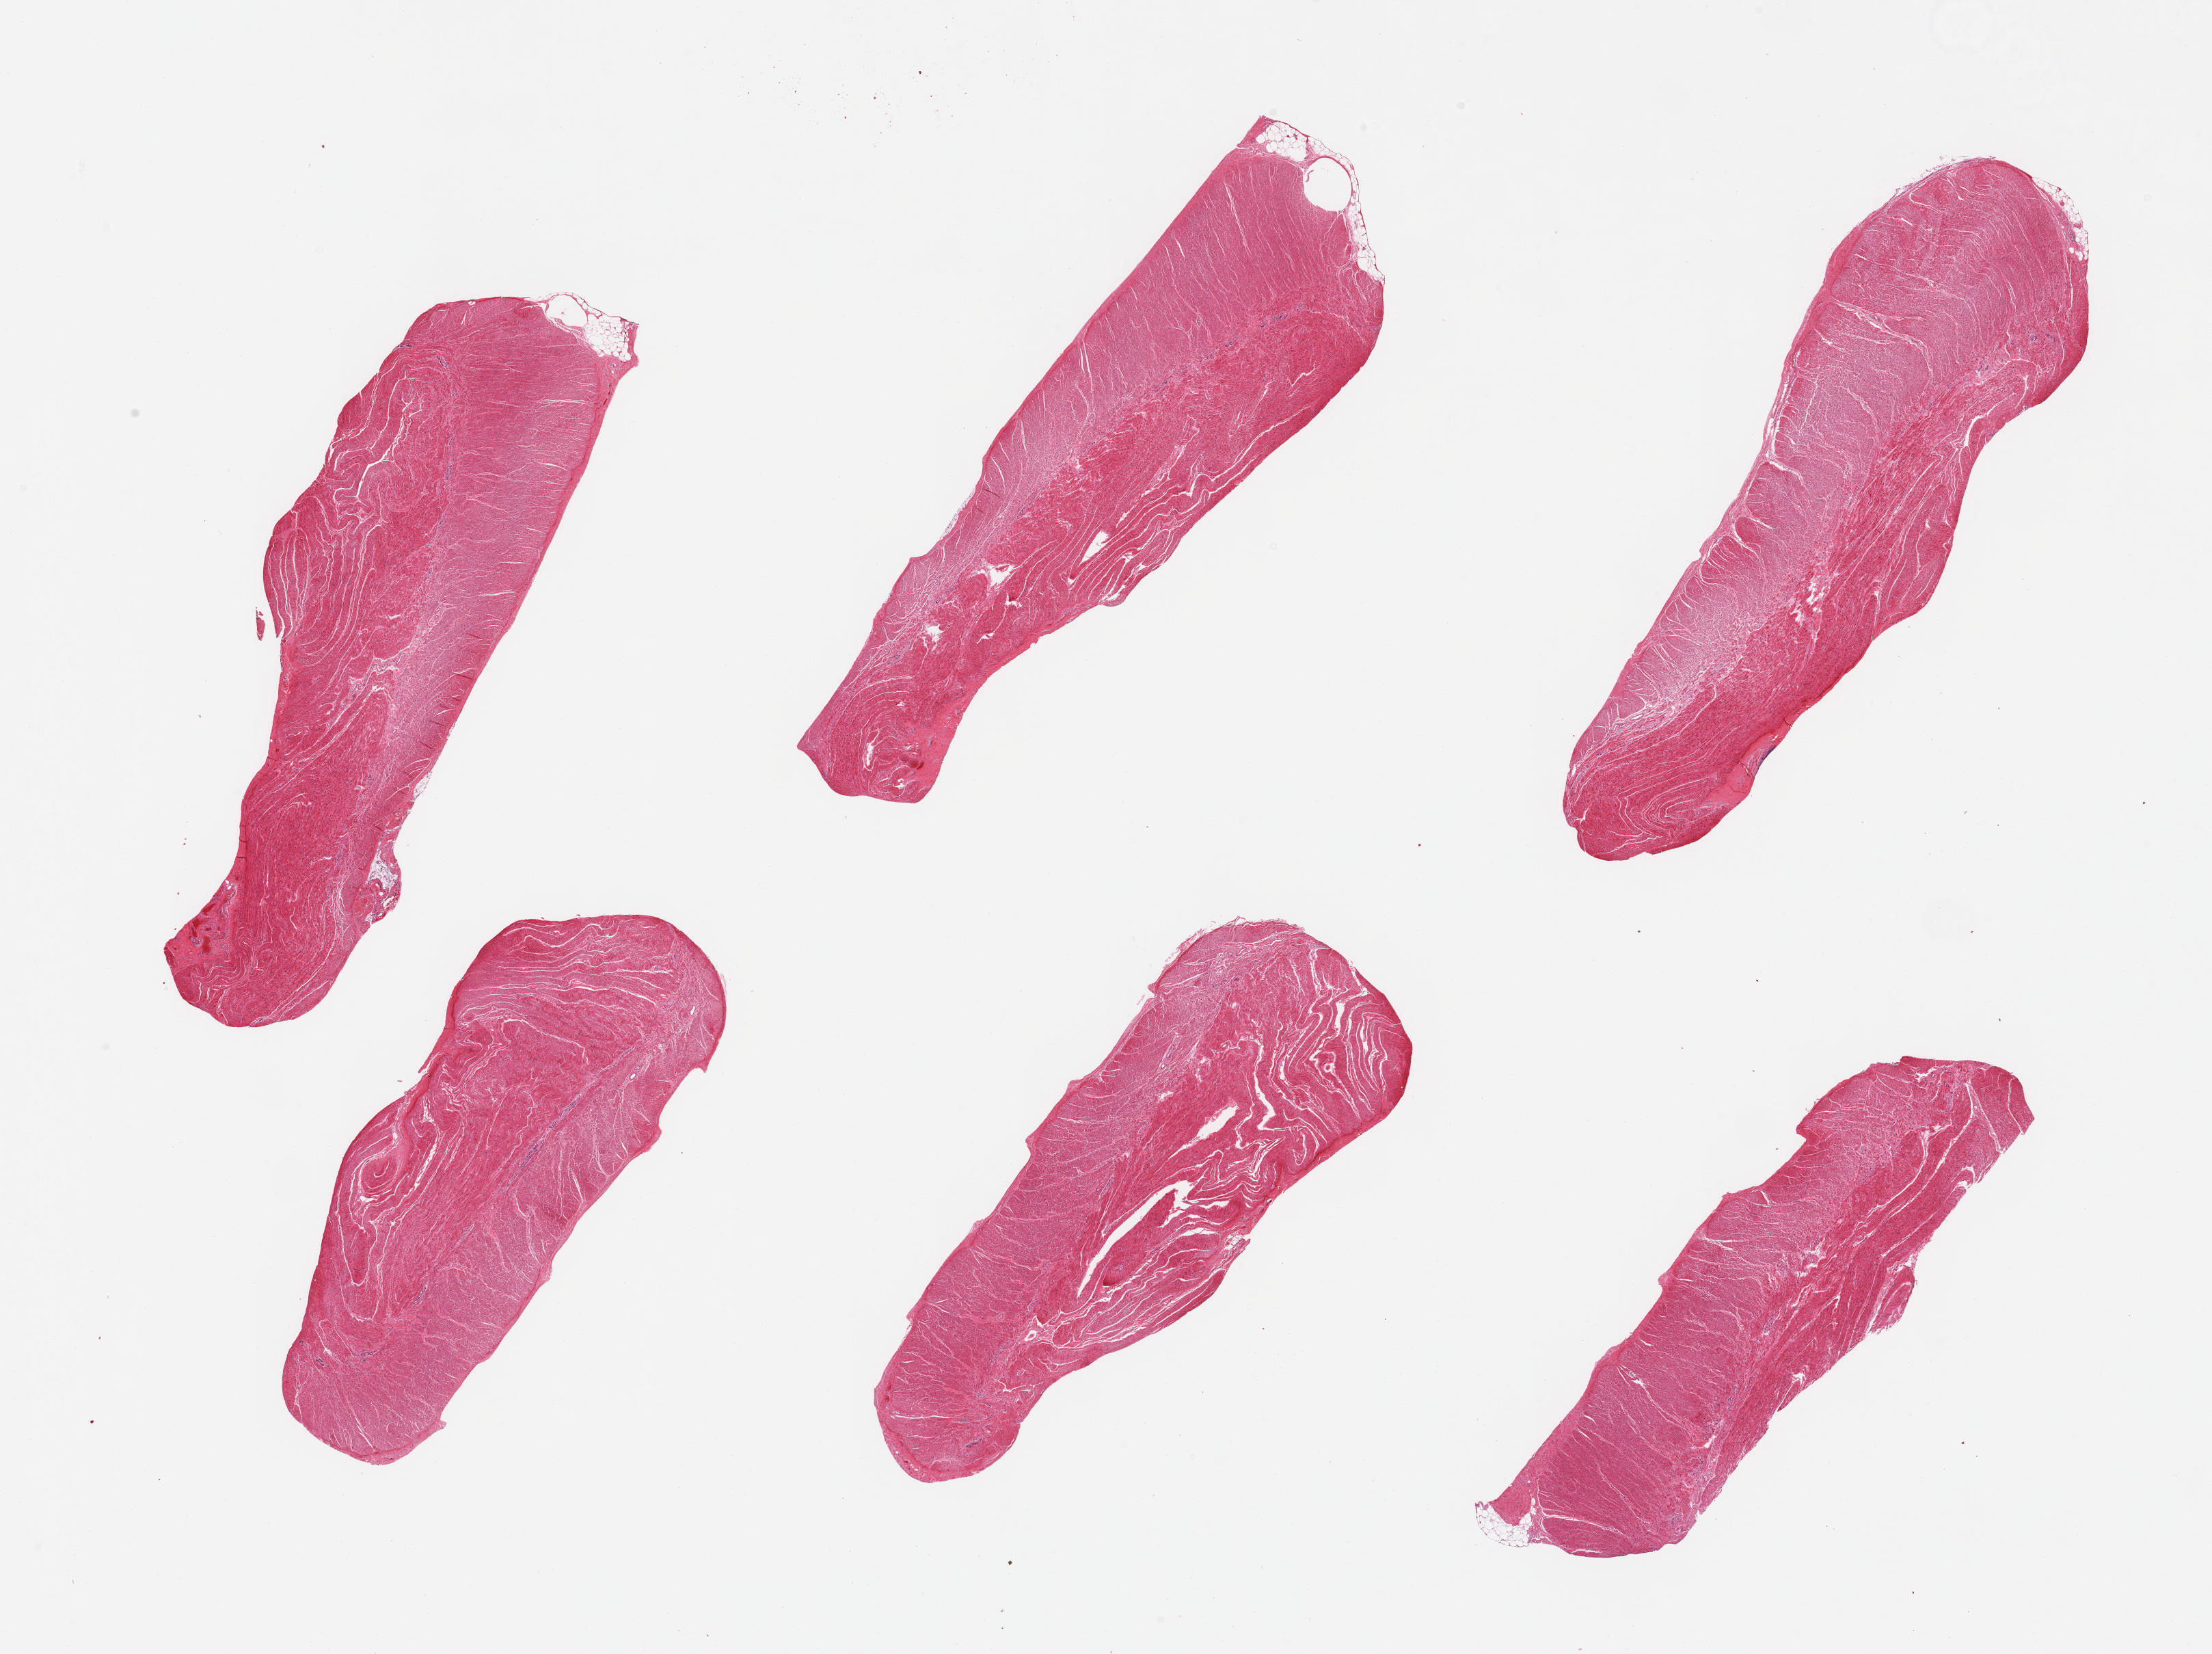
Haematoxylin and eosin whole-slide image, low-resolution overview of the scanned area, about 25.6 x 19.1 mm; PAXgene-fixed paraffin-embedded (PFPE) section; target tissue: sigmoid colon; donor tissue sample. Male donor.
Reviewer comment on this tissue sample: 6 pieces; well dissected muscularis.